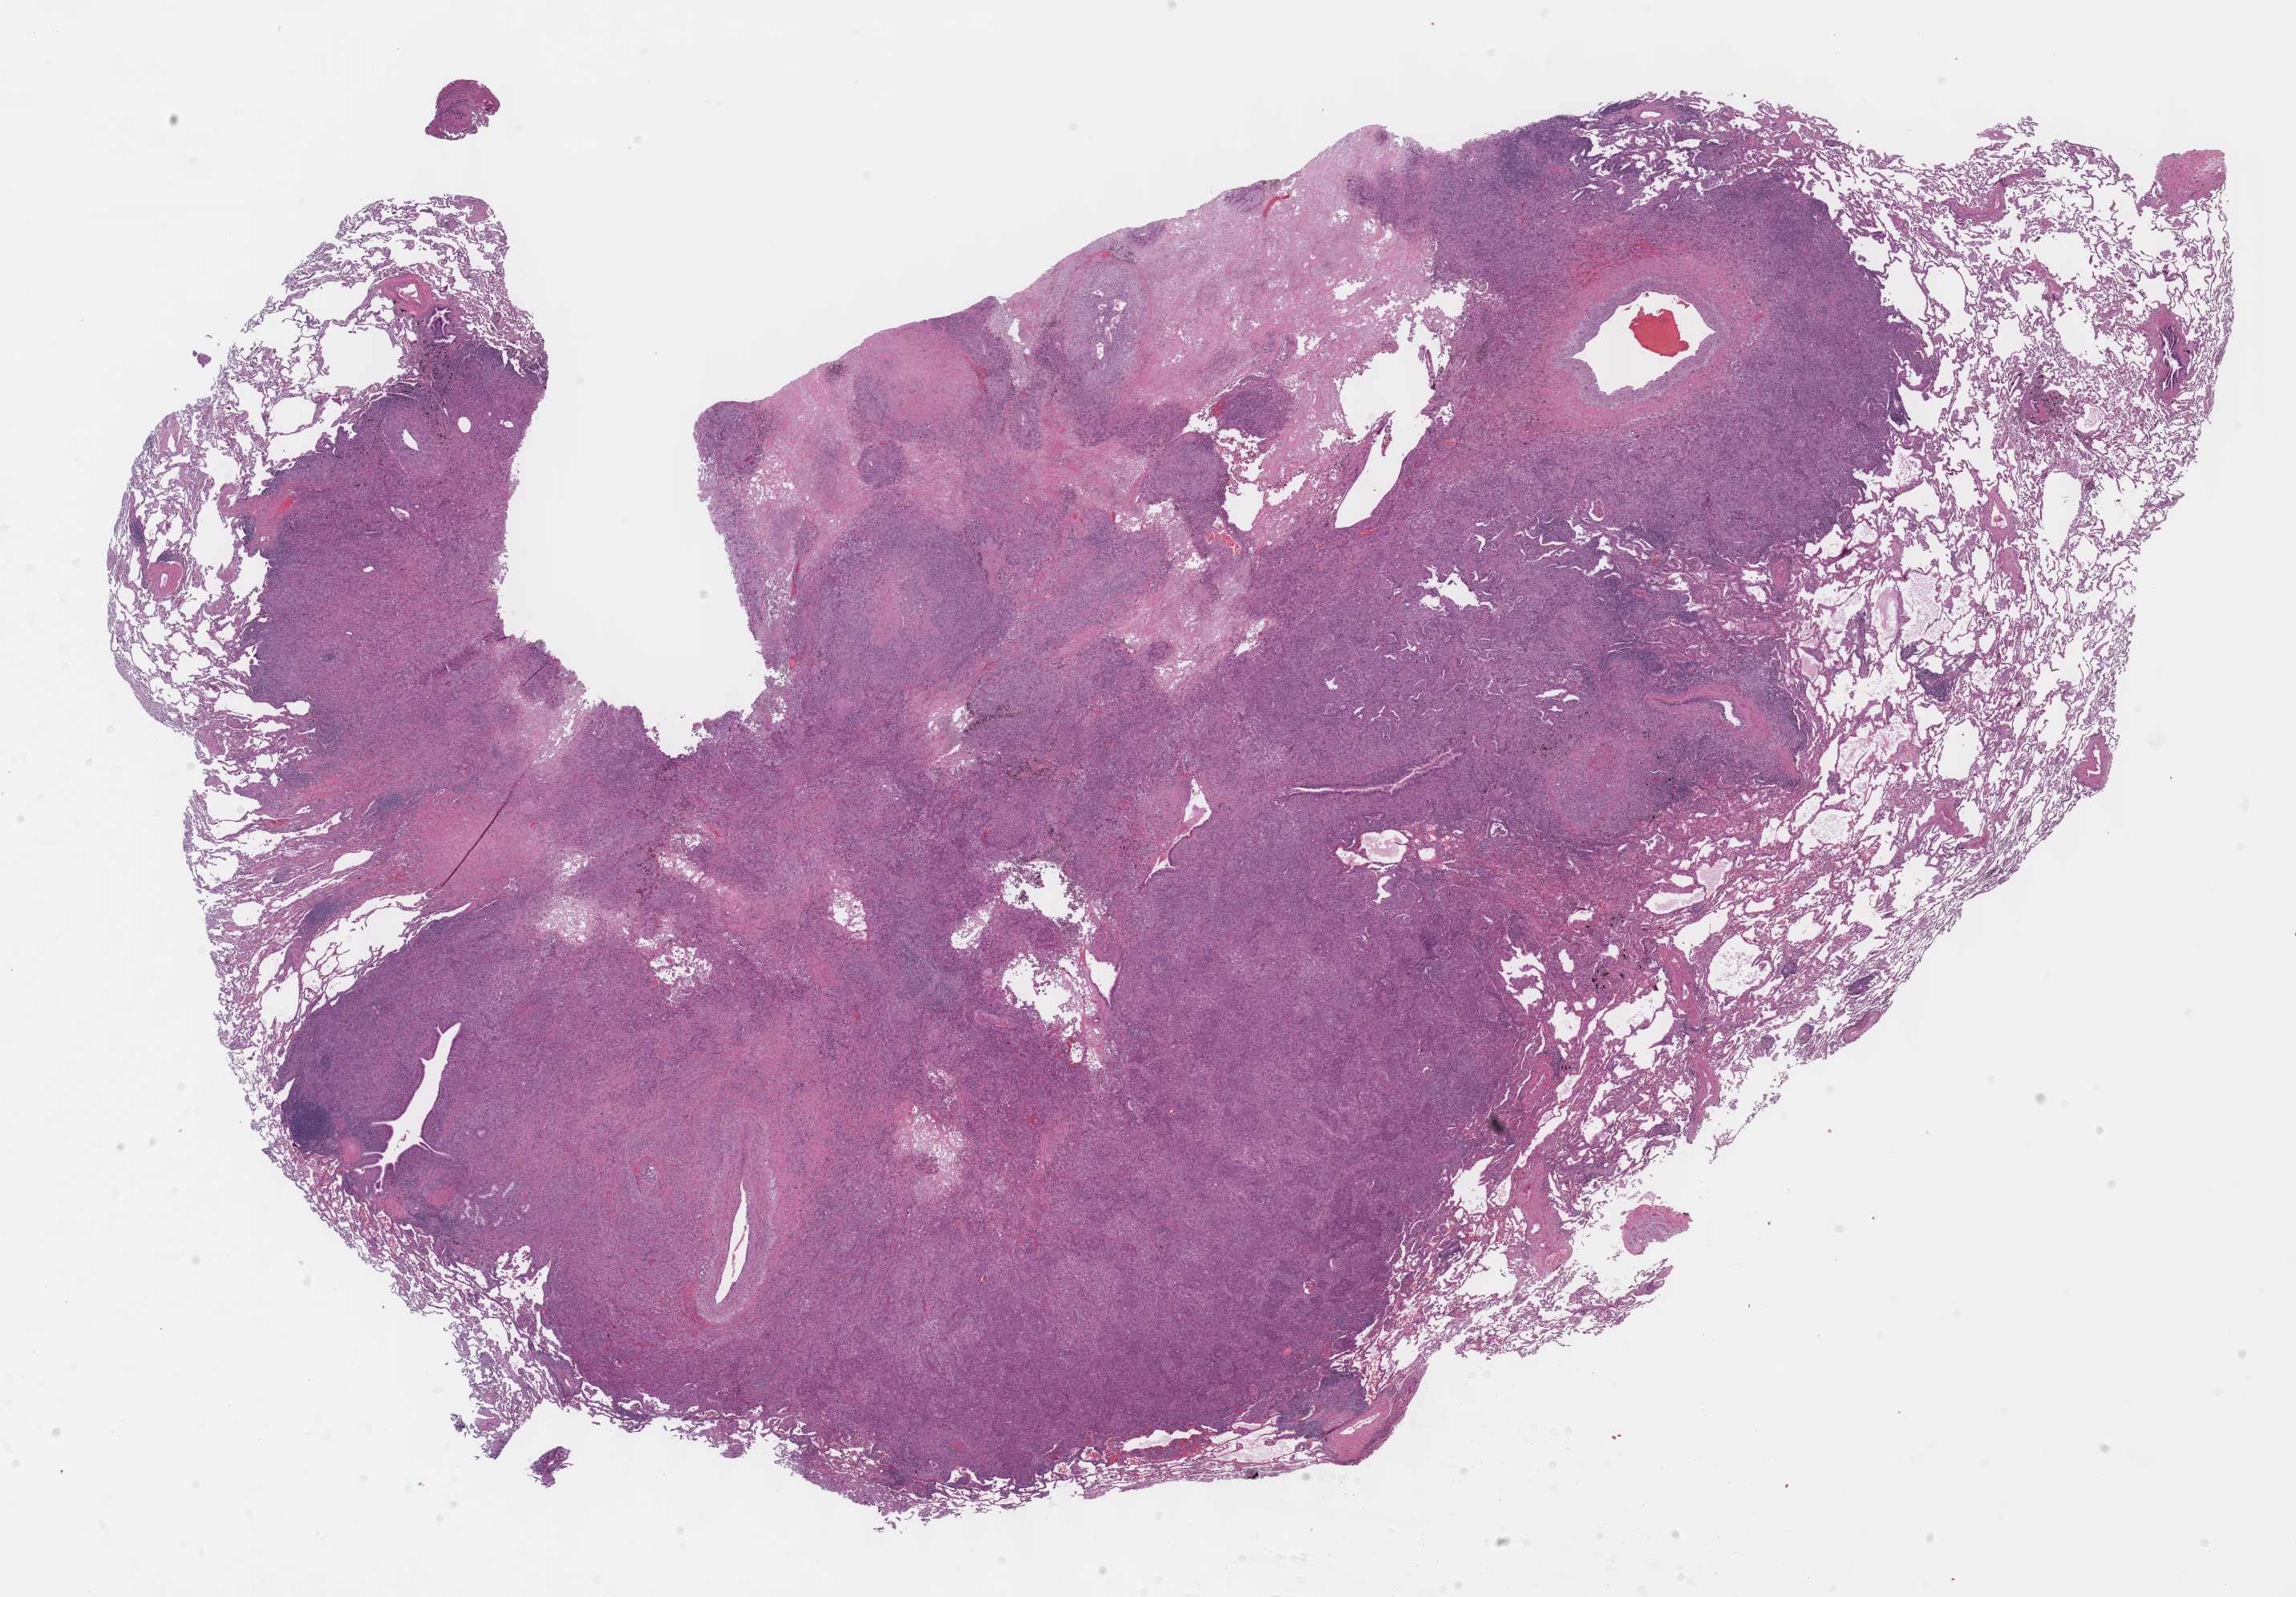
Whole-slide histology image, H&E-stained, a low-resolution overview of the entire scanned area, about 23.1 x 16.1 mm (acquisition: 40x scan), formalin-fixed paraffin-embedded (FFPE) diagnostic section, lung, primary tumour sample. Male, age 72 years at initial diagnosis.
* AJCC pathologic stage: IIA (7th edition)
* pathologic diagnosis: Adenocarcinoma, NOS (lower lobe, lung)
* laterality: right